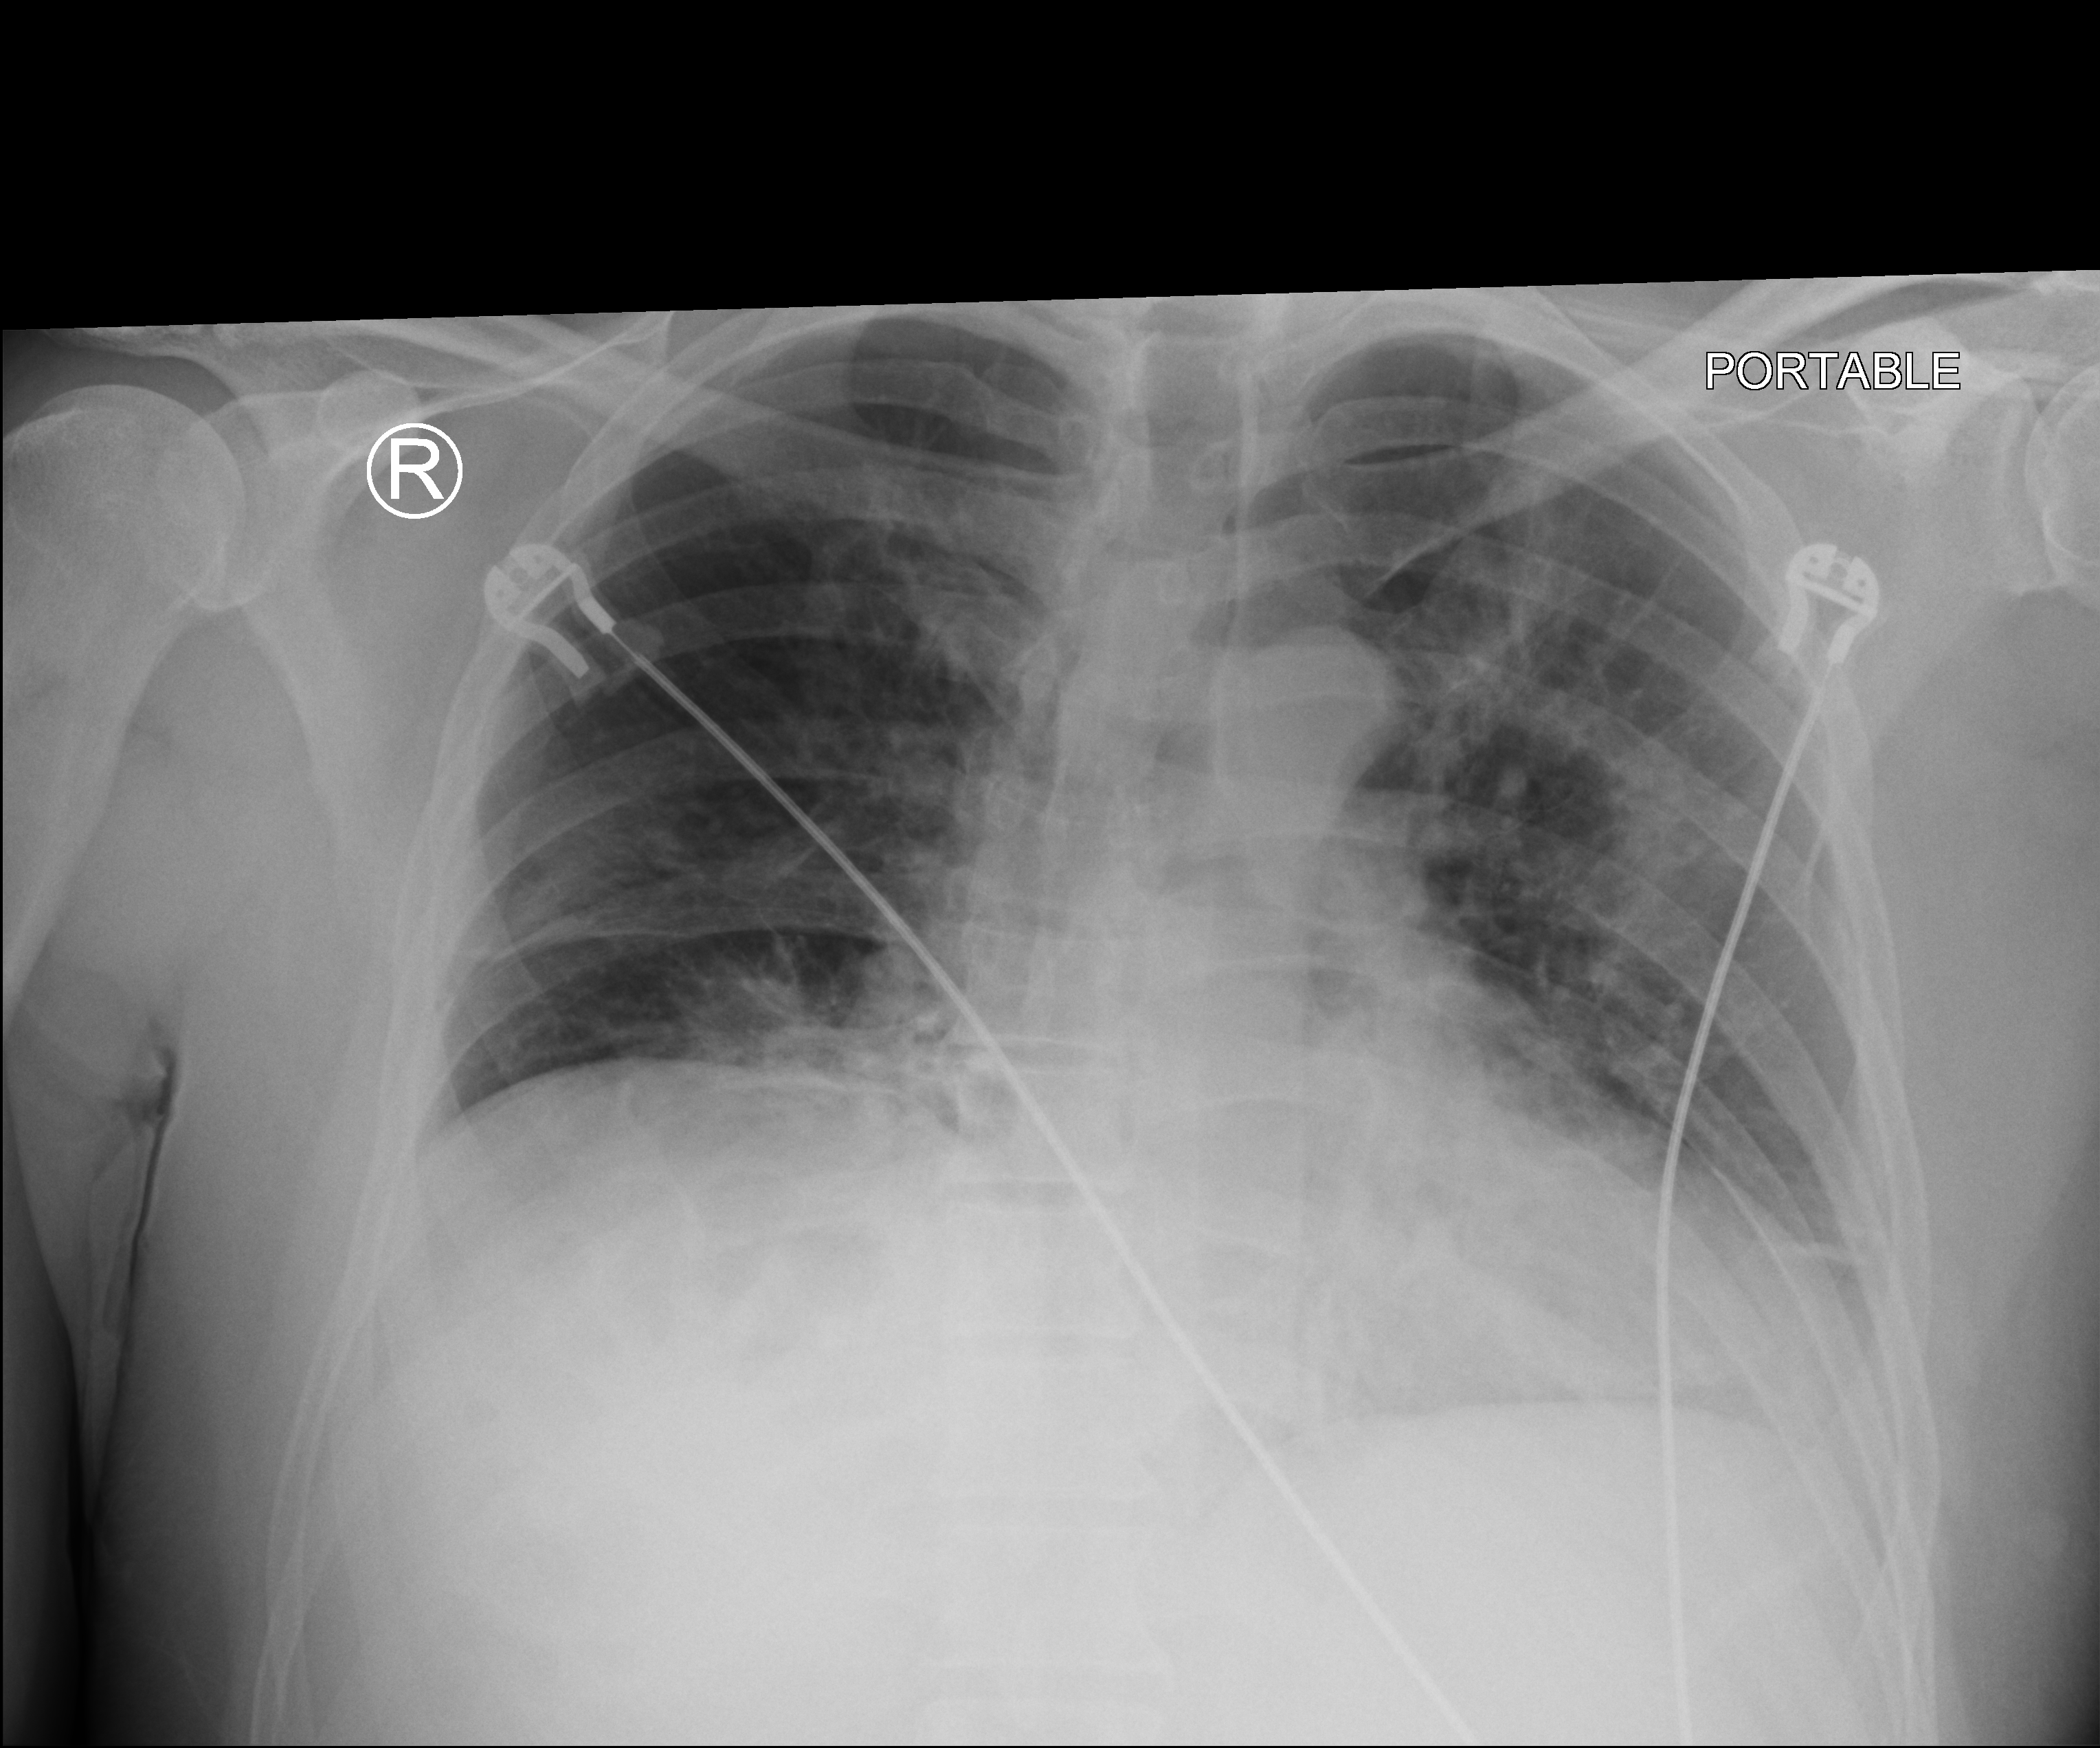
Chest X-ray (portable), anteroposterior (AP) projection. Patient hospitalised with COVID-19; male, aged 18–59 years.
Hospital-stay facts (about this admission, not read from this image; timing relative to this image not recorded): admitted to intensive care during this hospital stay: no; mechanically ventilated during this hospital stay: no.